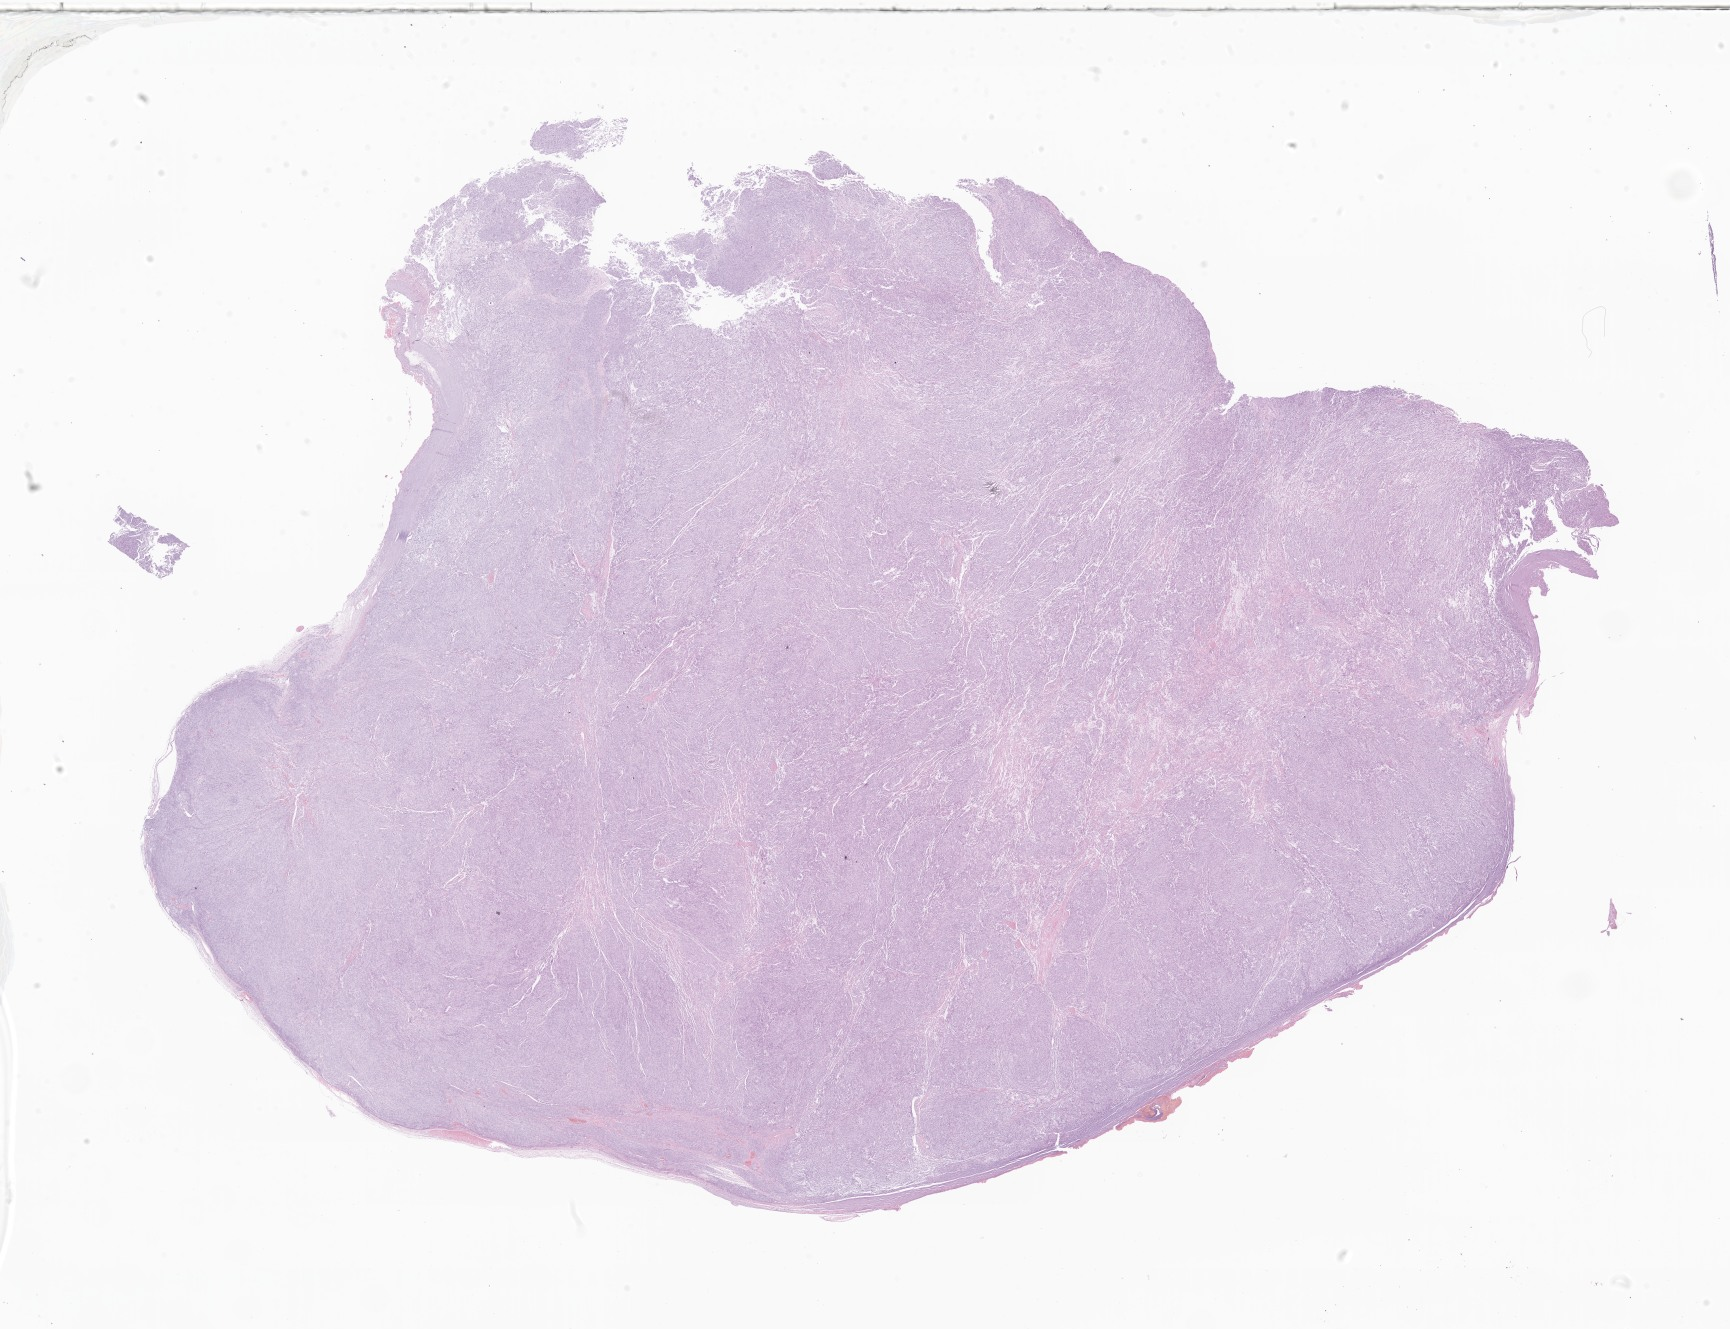
Hematoxylin and eosin (H&E) whole-slide image of tumor tissue from the brain, whole scanned area (about 29.2 x 22.4 mm) shown as a low-resolution overview; formalin-fixed, paraffin-embedded (FFPE) tissue. Female patient, age 202 months.
Recorded diagnosis: Meningioma, NOS.